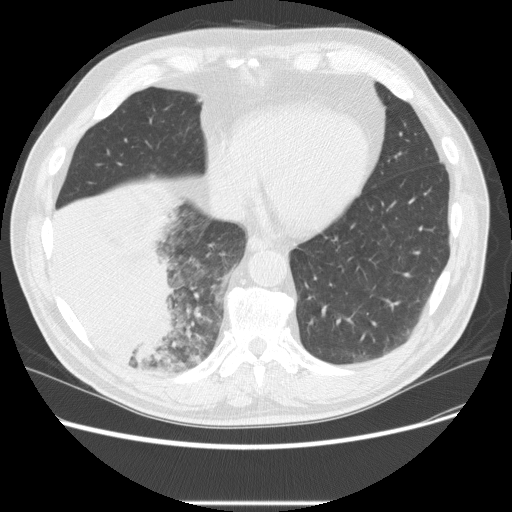
Low-dose screening chest CT, one axial slice. Slice 68 of 233 in the series (ordered by position). Reconstruction kernel STANDARD. 120 kVp. Lung window (W 1500 / L -600 HU). 512 × 512 image matrix, field of view 380 × 380 mm.
Outlined on this slice (outlined manually by an expert reader):
- lesion 3 (tumor, lower lobe of right lung): bounding box (x1, y1, x2, y2) in pixels: (51, 196, 177, 367)